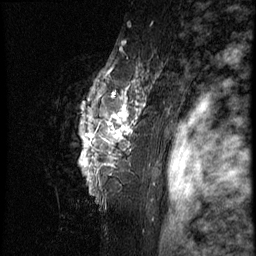
Breast MRI (dynamic contrast-enhanced), one sagittal slice; position 58 of 66 along the scan axis; 3 images stored at this slice position (order not interpretable as contrast timing); 1.5 T; TE 4.2 ms, TR 8.9 ms; 256 × 256 image matrix. Patient: female, 39 years. Case-level facts recorded for this patient, not image findings: setting: breast cancer imaged before/during neoadjuvant chemotherapy; receptor status: HER2-positive.
Annotated regions visible in this slice (semi-automatically segmented with operator editing):
- analysis volume of interest (the breast-tissue region the enhancement analysis was run in; not a lesion): bounding box [x1, y1, x2, y2] px = [55, 44, 166, 196]
- tumour enhancement mask (voxels above the 140 % enhancement threshold inside the analysis volume of interest): [89, 81, 145, 142]